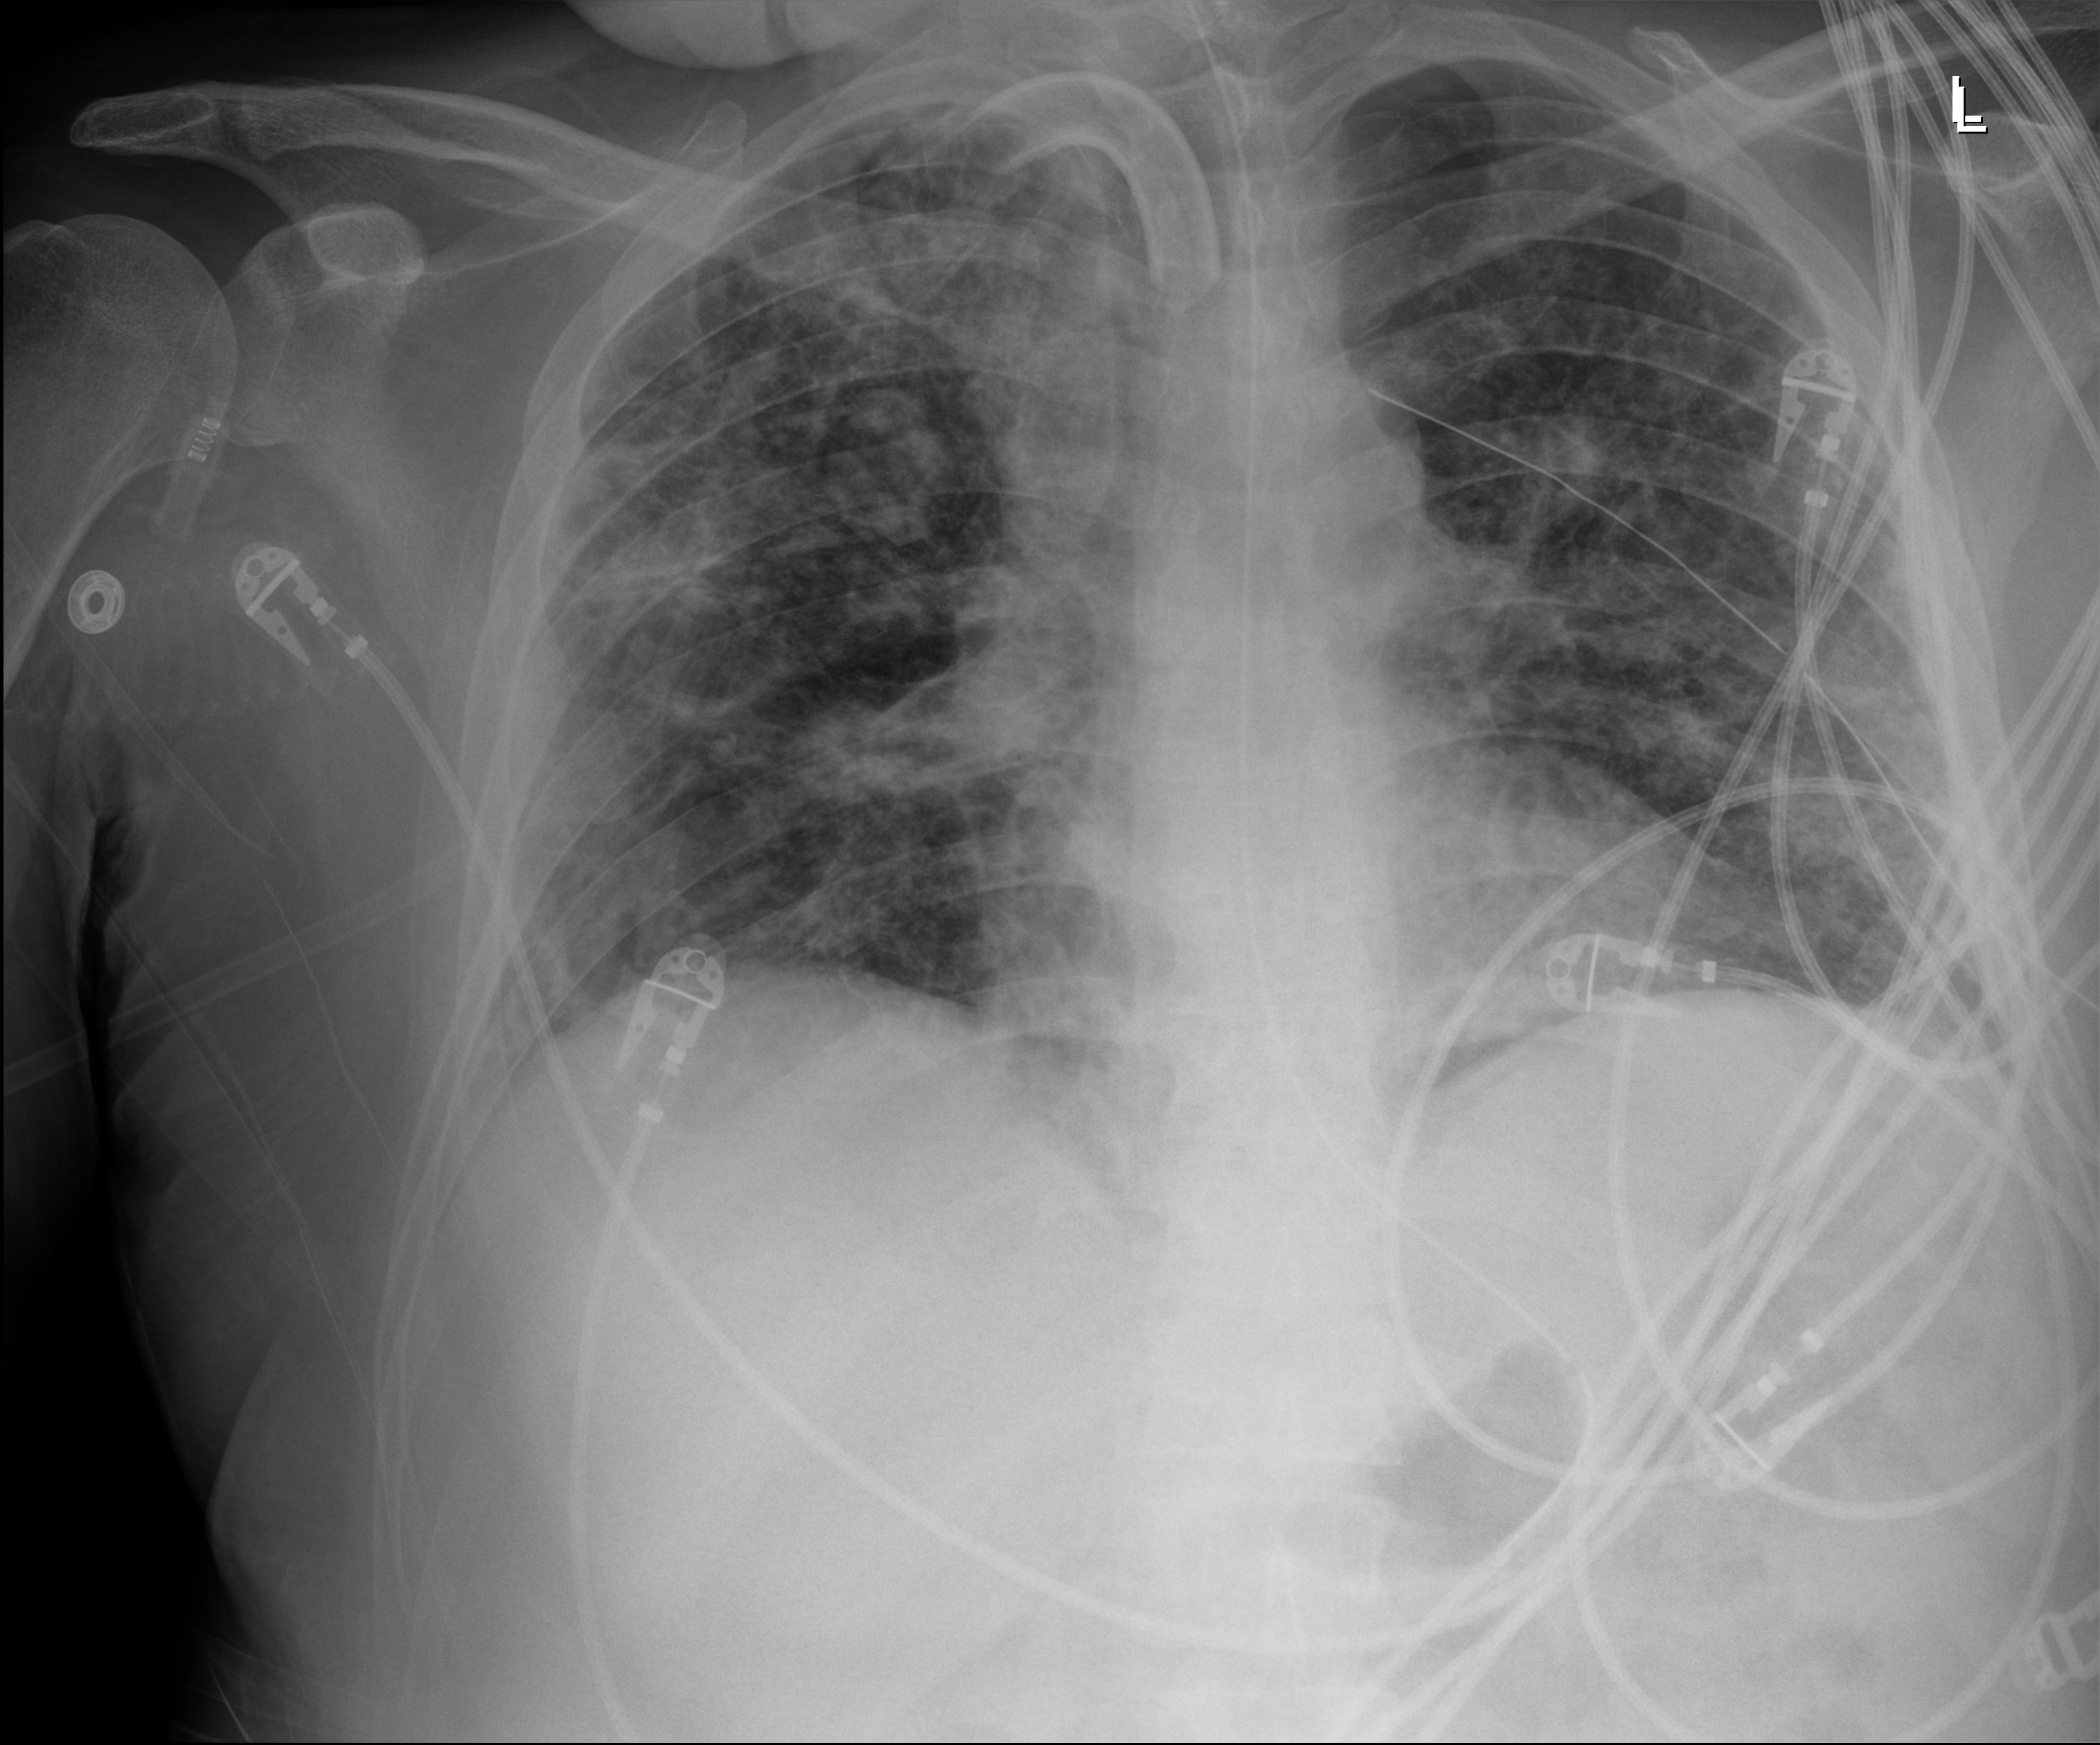
Bedside chest radiograph (digital radiography), anteroposterior (AP) projection. Male patient hospitalised with COVID-19, age 18–59 years.
Hospital-stay facts (about this admission, not read from this image; timing relative to this image not recorded): length of hospital stay: 63 days; mechanically ventilated during this hospital stay: yes; admitted to intensive care during this hospital stay: yes.